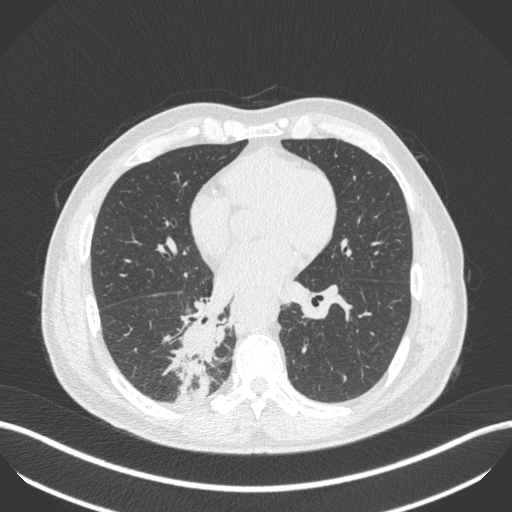
Chest CT, one axial slice. Slice 217 of 451 in the series (ordered by position). Reconstruction kernel B31f. 100 kVp. Lung window (W 1500 / L -600 HU). 1 mm slice thickness. 512 × 512 image matrix, field of view 400 × 400 mm. Male patient, age 61 years. Case-level facts recorded for this patient, not image findings: clinical TNM (as recorded): T1 N0 M0; histopathological grade: G3.
Annotated regions visible in this slice (bounding box drawn by a radiologist):
- lung tumour (recorded histology: small cell carcinoma): bounding box (x1, y1, x2, y2) in pixels: (165, 311, 226, 409)